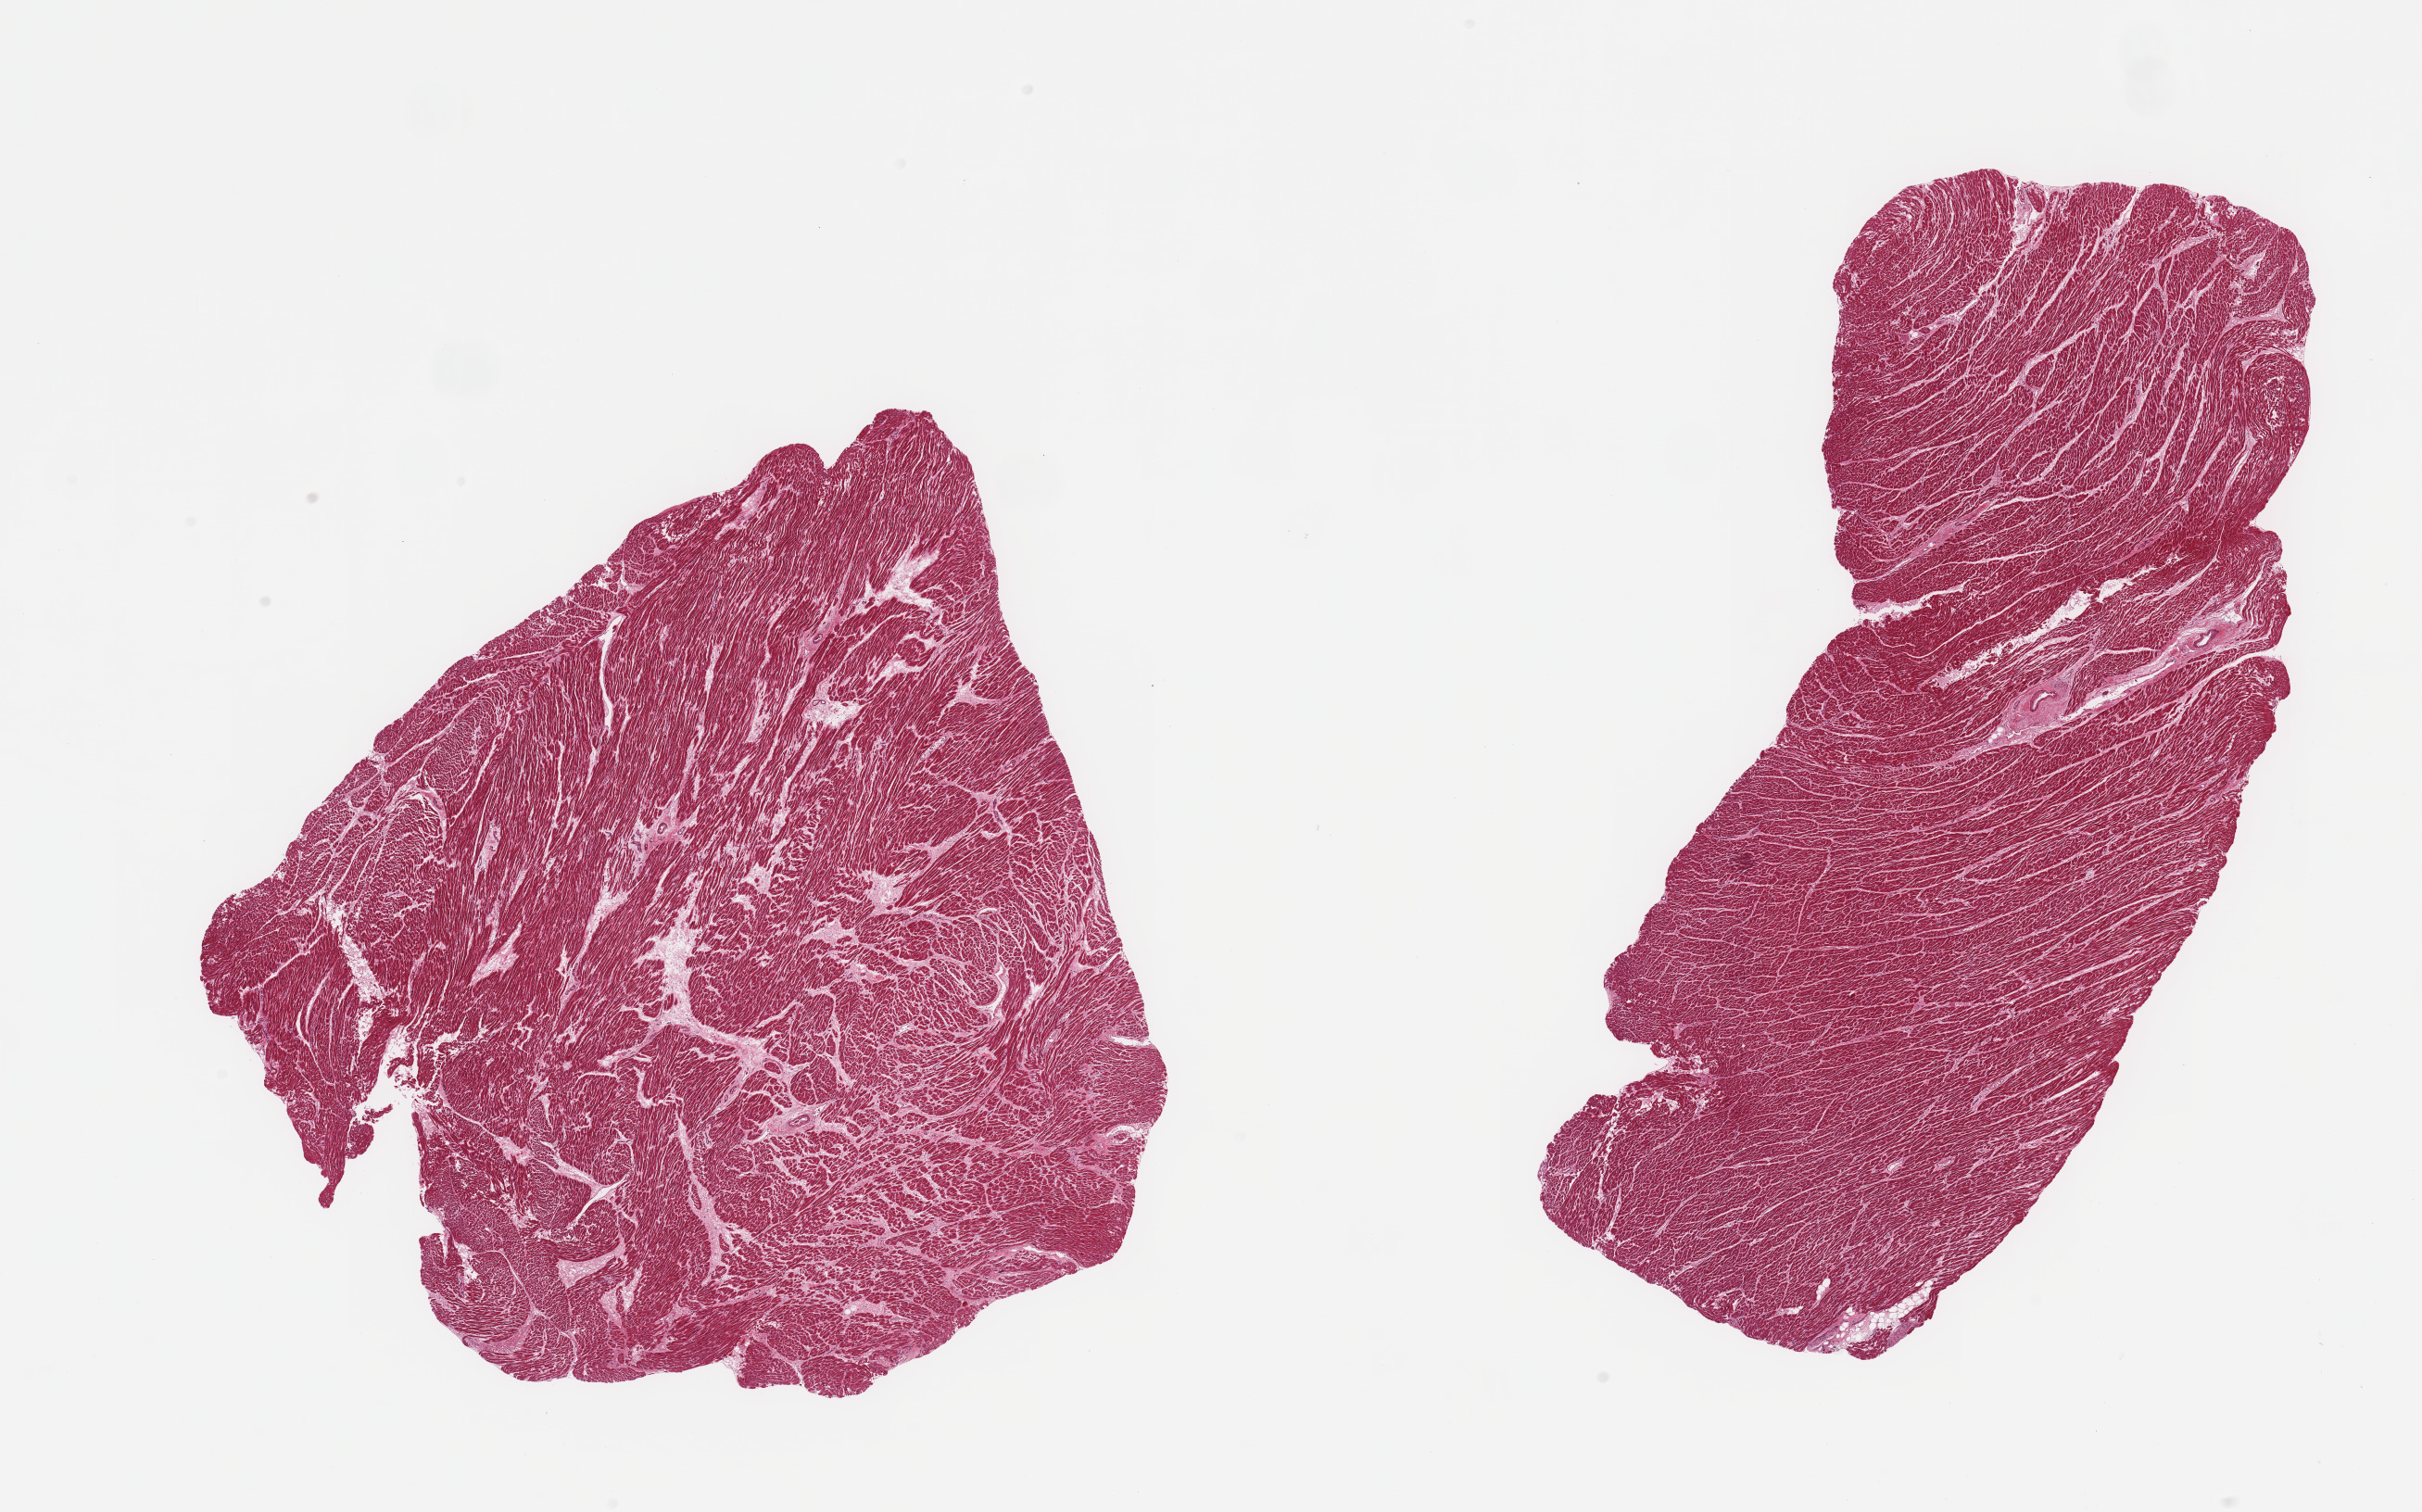
Whole-slide image, haematoxylin and eosin stain, a low-resolution overview of the entire scanned area, about 20.7 x 12.9 mm (acquisition: 20x scan). PAXgene-fixed paraffin-embedded (PFPE) section. Section of heart (target tissue). Donor tissue sample. Donor sex: male.
Review note (as recorded): 2 pieces, minimal interstitial fibrosis;ischemic change.